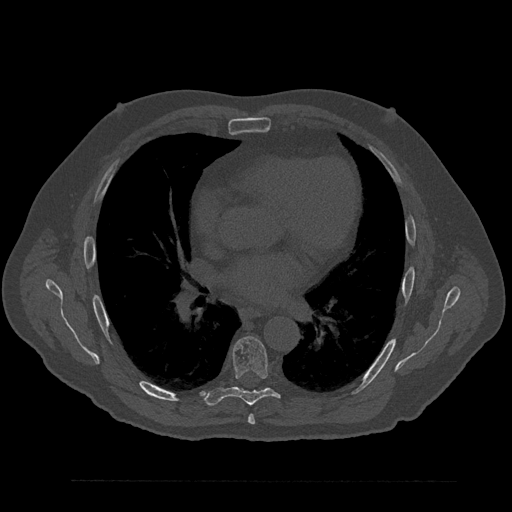
CT including the spine, one axial slice; slice 507 of 797 in the series (ordered by position); reconstruction kernel Br40s/3; bone window (W 1800 / L 400 HU); 0.5 mm slice thickness; 512 × 512 image matrix, field of view 430 × 430 mm. Patient: male, 61 years. From the clinical record (not read from this slice): primary cancer: prostate.
Structures marked on this image (semi-automatic segmentation, software-assisted and operator-edited):
- T6 vertebra: bounding box (x1, y1, x2, y2) in pixels: (248, 415, 255, 425)
- T7 vertebra: (204, 336, 281, 406)